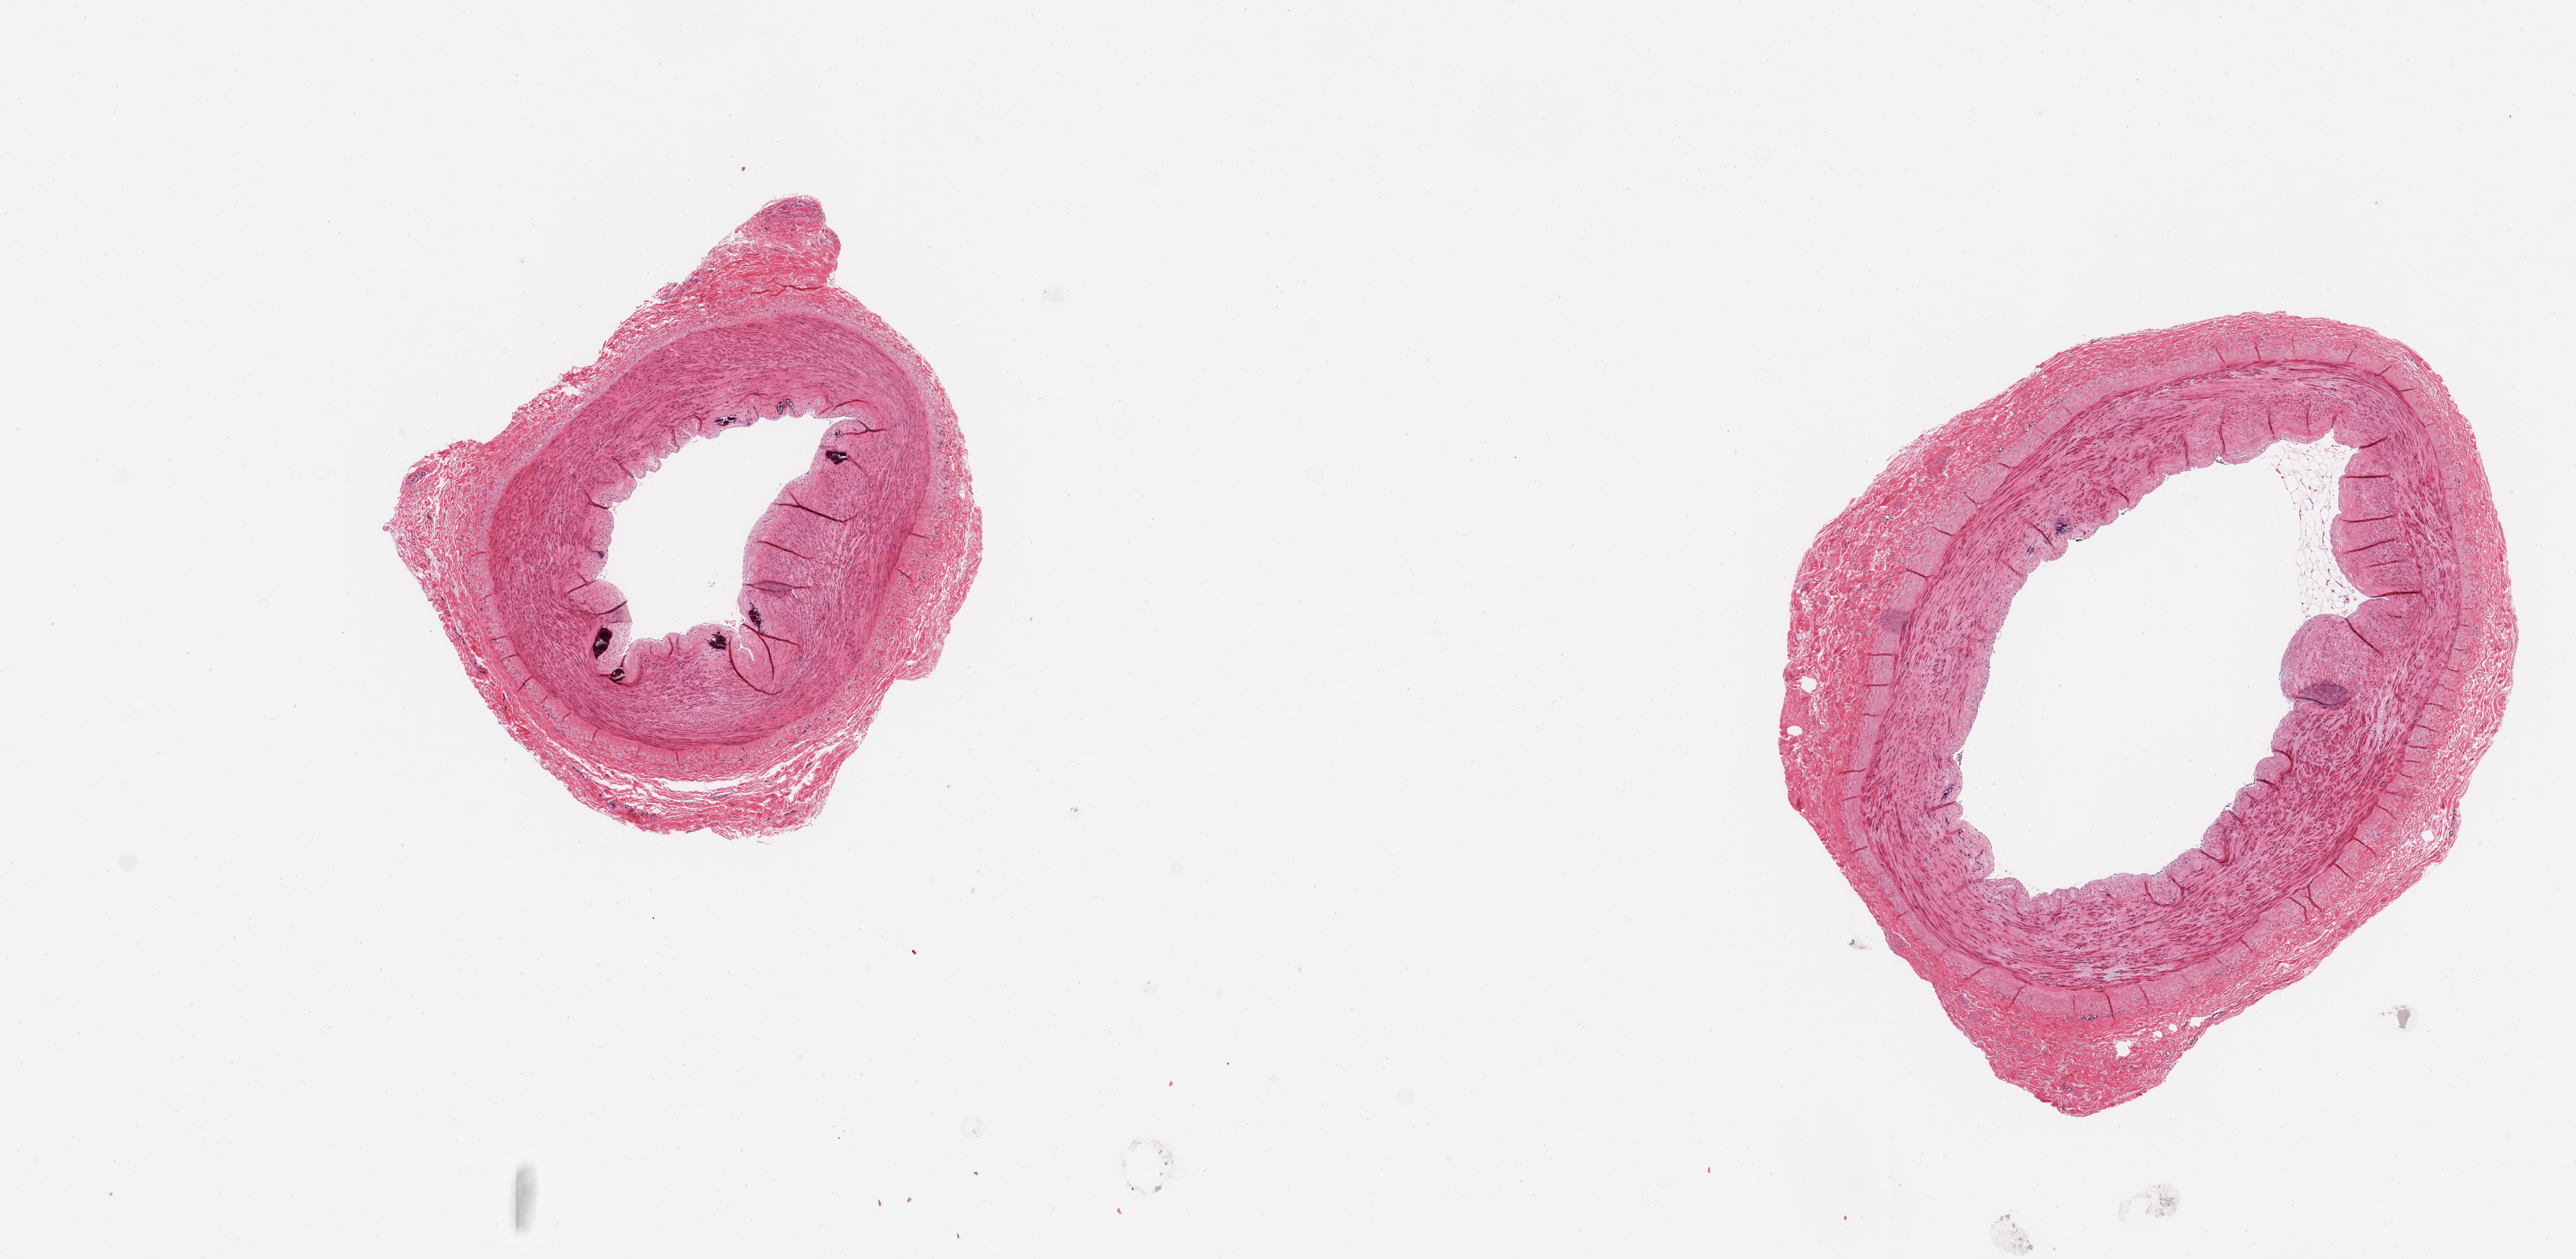
Hematoxylin and eosin (H&E) whole-slide image — low-resolution overview of the scanned area, about 14.8 x 7.2 mm (acquisition: 20x scan); PAXgene-fixed, paraffin-embedded tissue; target tissue: tibial artery; donor tissue sample. Donor: female.
Reviewer comment on this tissue sample: 2 pieces, no significant adherent fat or atherosis; focal Monckeberg medial sclerosis.